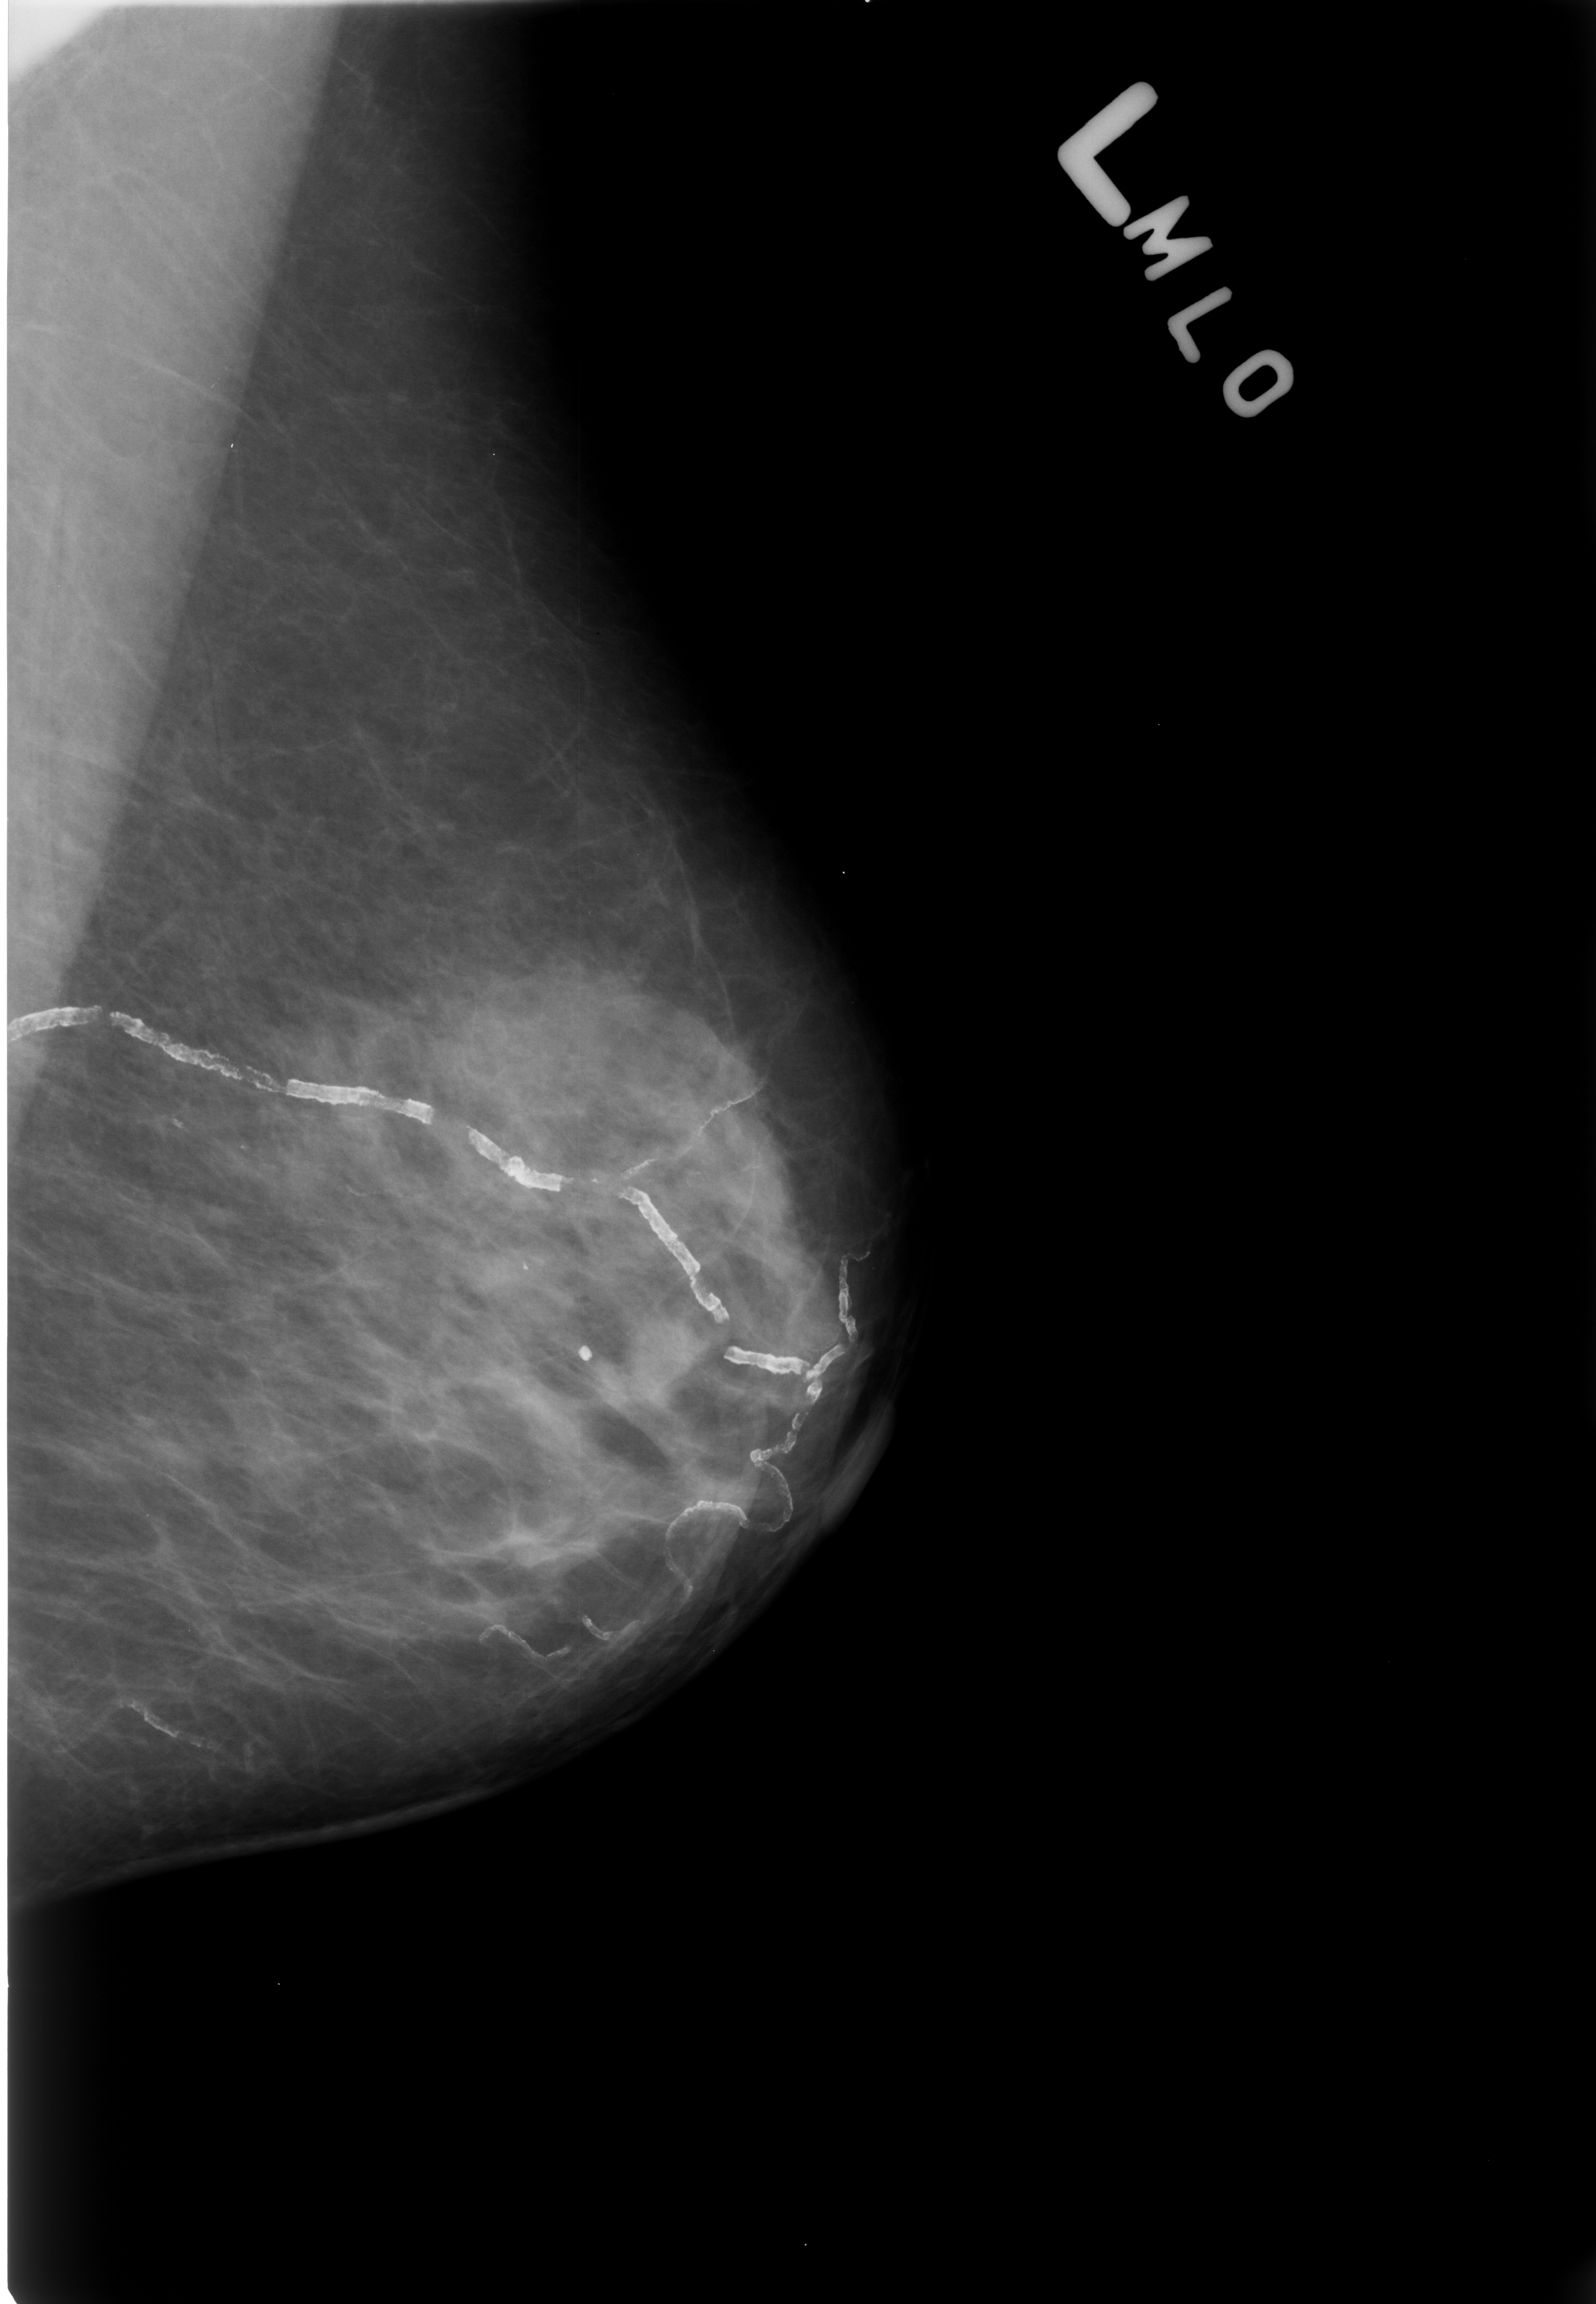
Digitized screen-film mammogram; left breast; MLO view; 1596 × 2304 image matrix.
Marked abnormalities (boxes around the expert regions of interest):
- calcifications, morphology vascular; BI-RADS assessment category 2; outcome (as recorded, no biopsy): benign without callback (not worked up further): bounding box (x1, y1, x2, y2) in pixels: (4, 999, 865, 1408)